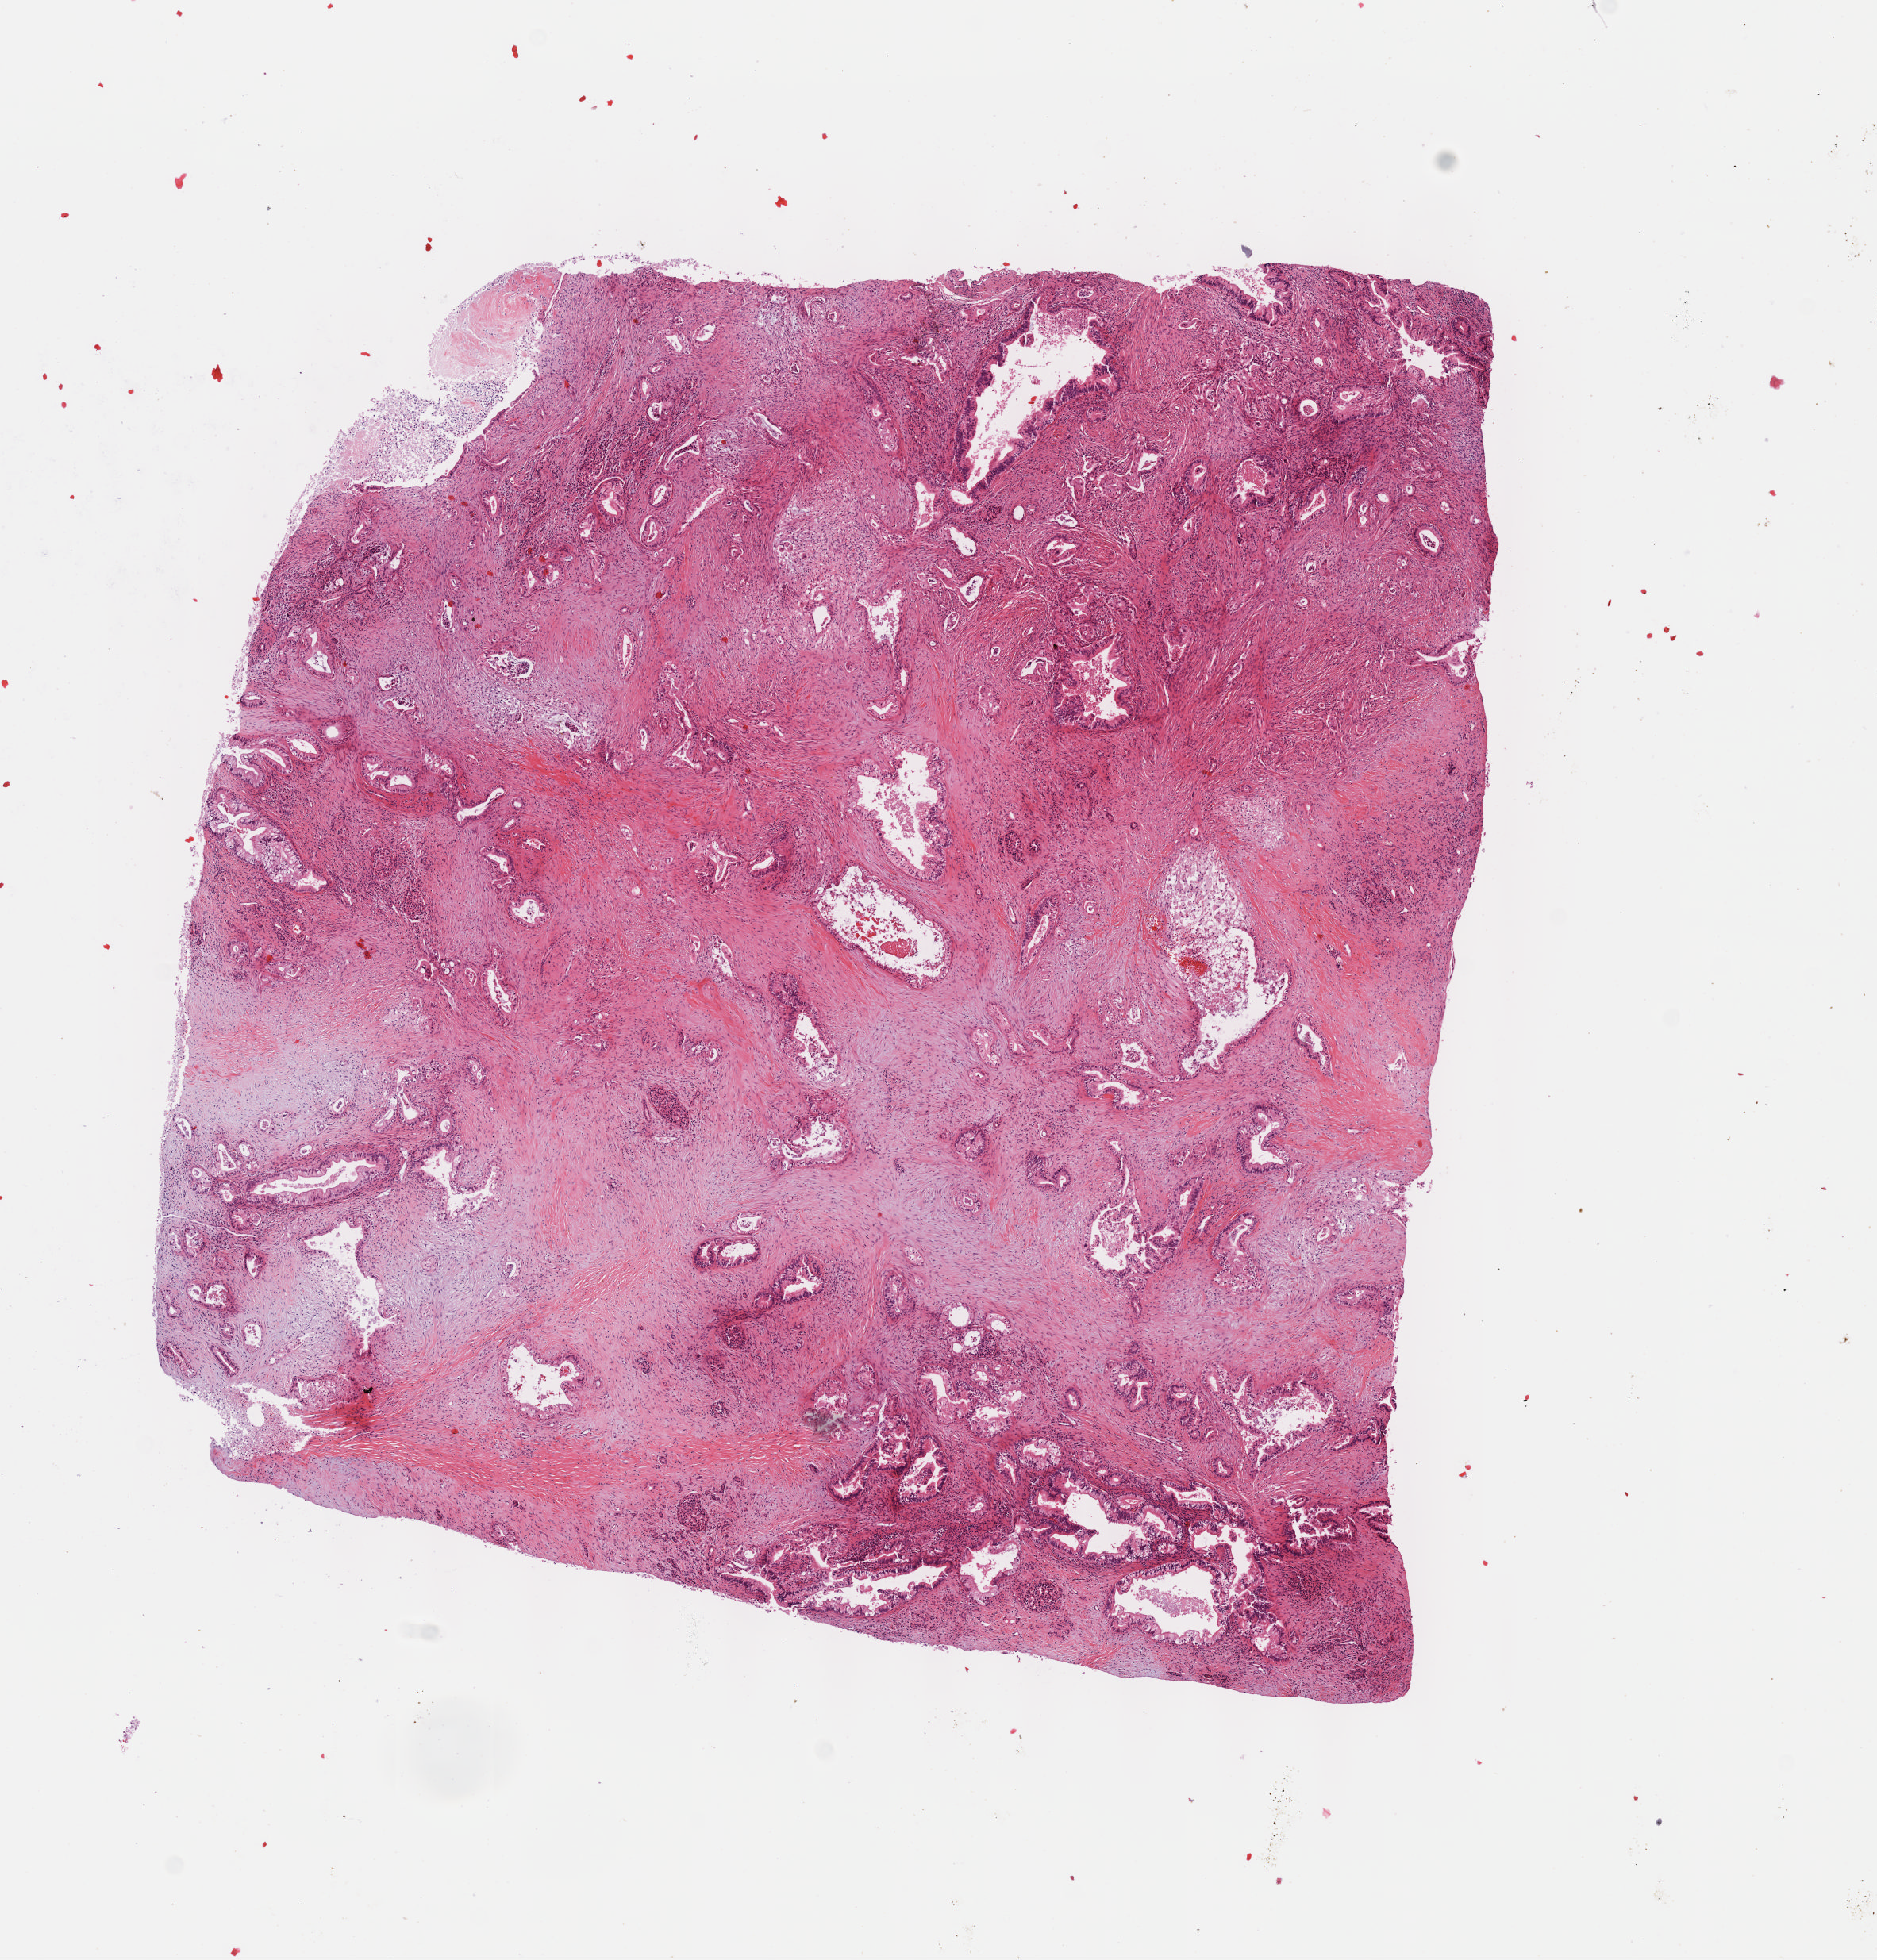
H&E whole-slide image — whole scanned area (about 9.6 x 10.0 mm) shown as a low-resolution overview; formalin-fixed paraffin-embedded (FFPE) diagnostic section; primary tumour sample from the pancreas. Female patient; age at initial diagnosis 75 years. Histologic grade: G2 (moderately differentiated).
* lymph nodes positive (case pathology): 3 of 11 examined
* AJCC pathologic stage: IIB (7th edition)
* diagnosis: Infiltrating duct carcinoma, NOS (body of pancreas)